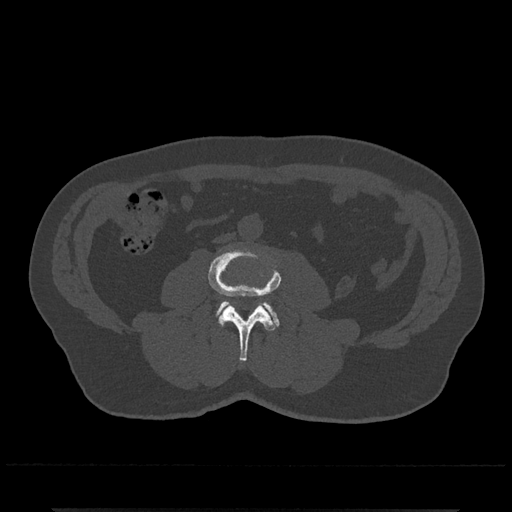
CT including the spine, one axial slice; bone window (W 1800 / L 400 HU); 0.5 mm slice thickness; 512 × 512 image matrix. Patient: male, 67 years. Case-level facts recorded for this patient, not image findings: primary cancer: prostate.
Outlined on this slice (semi-automatic segmentation, software-assisted and operator-edited):
- L3 vertebra: bounding box [x1, y1, x2, y2] px = [208, 249, 281, 362]
- L4 vertebra: [216, 300, 279, 326]